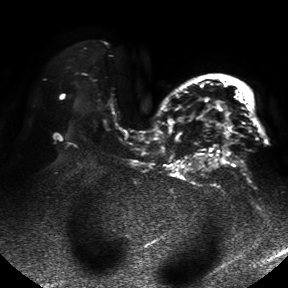
Breast MRI, one axial slice; position 33 of 50 along the scan axis; diffusion-weighted series; image 2 of 4 stored at this slice position (different b-values; order by instance number); 1.5 T; 4 mm slice thickness; 288 × 288 image matrix. Female patient.
Annotated regions visible in this slice (expert manual segmentation):
- tumour on diffusion-weighted imaging: bounding box <219,102,226,110> (left, top, right, bottom; pixels)